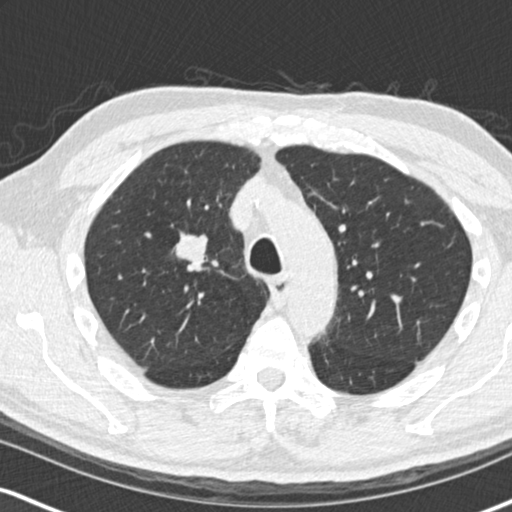
Low-dose screening chest CT, one axial slice; position 112 of 170 along the scan axis; 120 kVp; lung window (W 1500 / L -600 HU); 2 mm slice thickness; 512 × 512 image matrix.
Annotated regions visible in this slice (expert manual segmentation):
- lesion 1 (tumor, upper lobe of right lung): bounding box <176,234,206,261> (left, top, right, bottom; pixels)